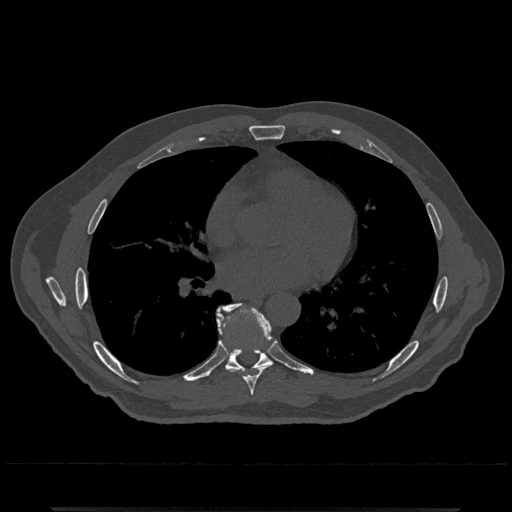
CT including the spine, one axial slice. Slice 696 of 797 in the series (ordered by position). Reconstruction kernel Br40s/3. Bone window (W 1800 / L 400 HU). 0.5 mm slice thickness. 512 × 512 image matrix. Male patient, age 67 years. From the clinical record (not read from this slice): primary cancer: prostate.
Outlined on this slice (semi-automatic segmentation, software-assisted and operator-edited):
- T7 vertebra: box from (x=218, y=322) to (x=272, y=396) px
- T8 vertebra: (x=216, y=303)–(x=271, y=372)